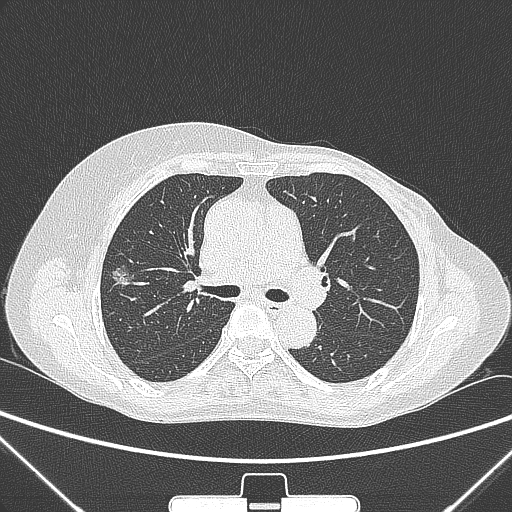
Chest CT, one axial slice. Lung window (W 1500 / L -600 HU). 1 mm slice thickness. 512 × 512 image matrix, field of view 350 × 350 mm. Patient: female, 64 years. Case-level facts recorded for this patient, not image findings: clinical TNM (as recorded): T1c N0 M0; histopathological grade: G1-2.
Outlined on this slice (rectangle marked by the reading radiologist):
- lung tumour (recorded histology: adenocarcinoma): bounding box <107,257,137,295> (left, top, right, bottom; pixels)